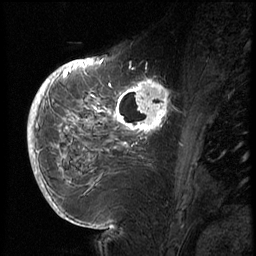
Breast MRI (dynamic contrast-enhanced), one sagittal slice. Position 25 of 72 along the scan axis. 3 images stored at this slice position (order not interpretable as contrast timing). 1.5 T. TE 4.2 ms, TR 8.9 ms. 256 × 256 image matrix, field of view 200 × 200 mm. Patient: female, 56 years. Case-level facts recorded for this patient, not image findings: setting: breast cancer imaged before/during neoadjuvant chemotherapy.
Annotated regions visible in this slice (semi-automatically segmented with operator editing):
- analysis volume of interest (the breast-tissue region the enhancement analysis was run in; not a lesion): box from (x=114, y=76) to (x=177, y=138) px
- tumour enhancement mask (voxels above the 140 % enhancement threshold inside the analysis volume of interest): (x=114, y=78)–(x=170, y=134)